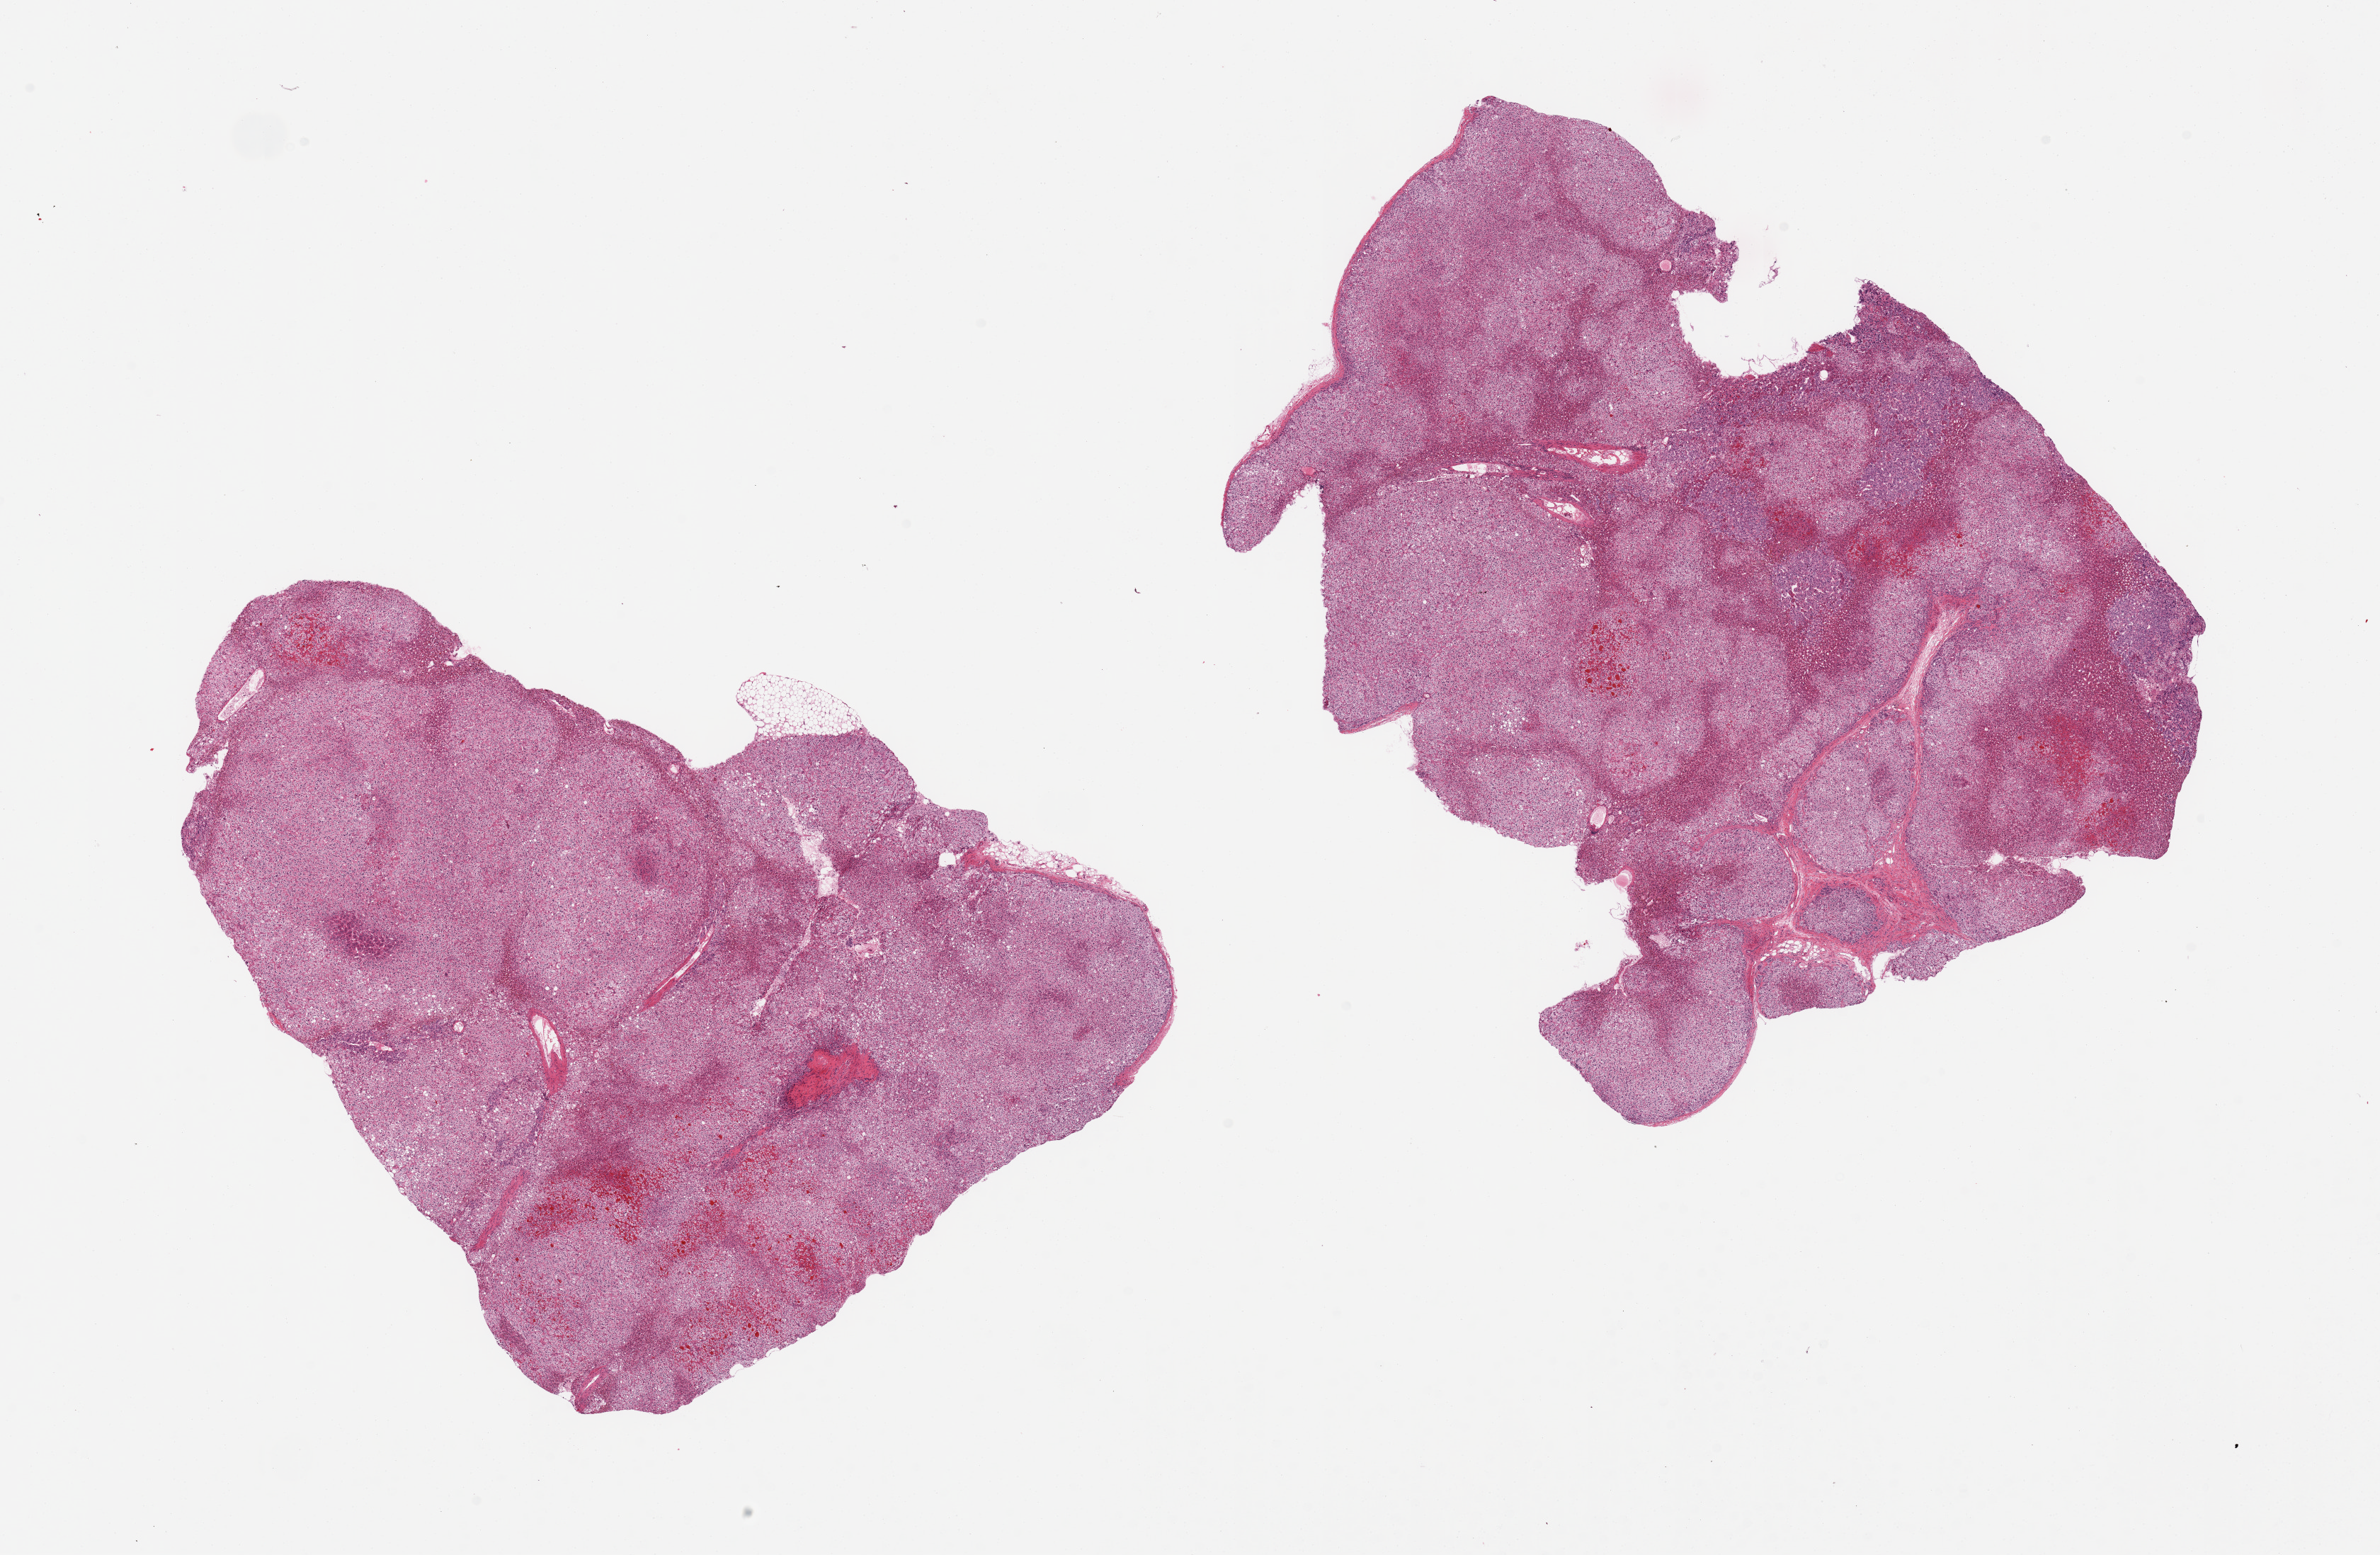
Whole-slide image, H&E stain, a low-resolution overview of the entire scanned area, about 26.6 x 17.4 mm (from a 20x scan), PAXgene-fixed paraffin-embedded (PFPE) section, sampled site (target tissue): adrenal gland, donor tissue sample. Donor sex: female.
Reviewer comment on this tissue sample: 2 pieces, all cortex, minimal fat.